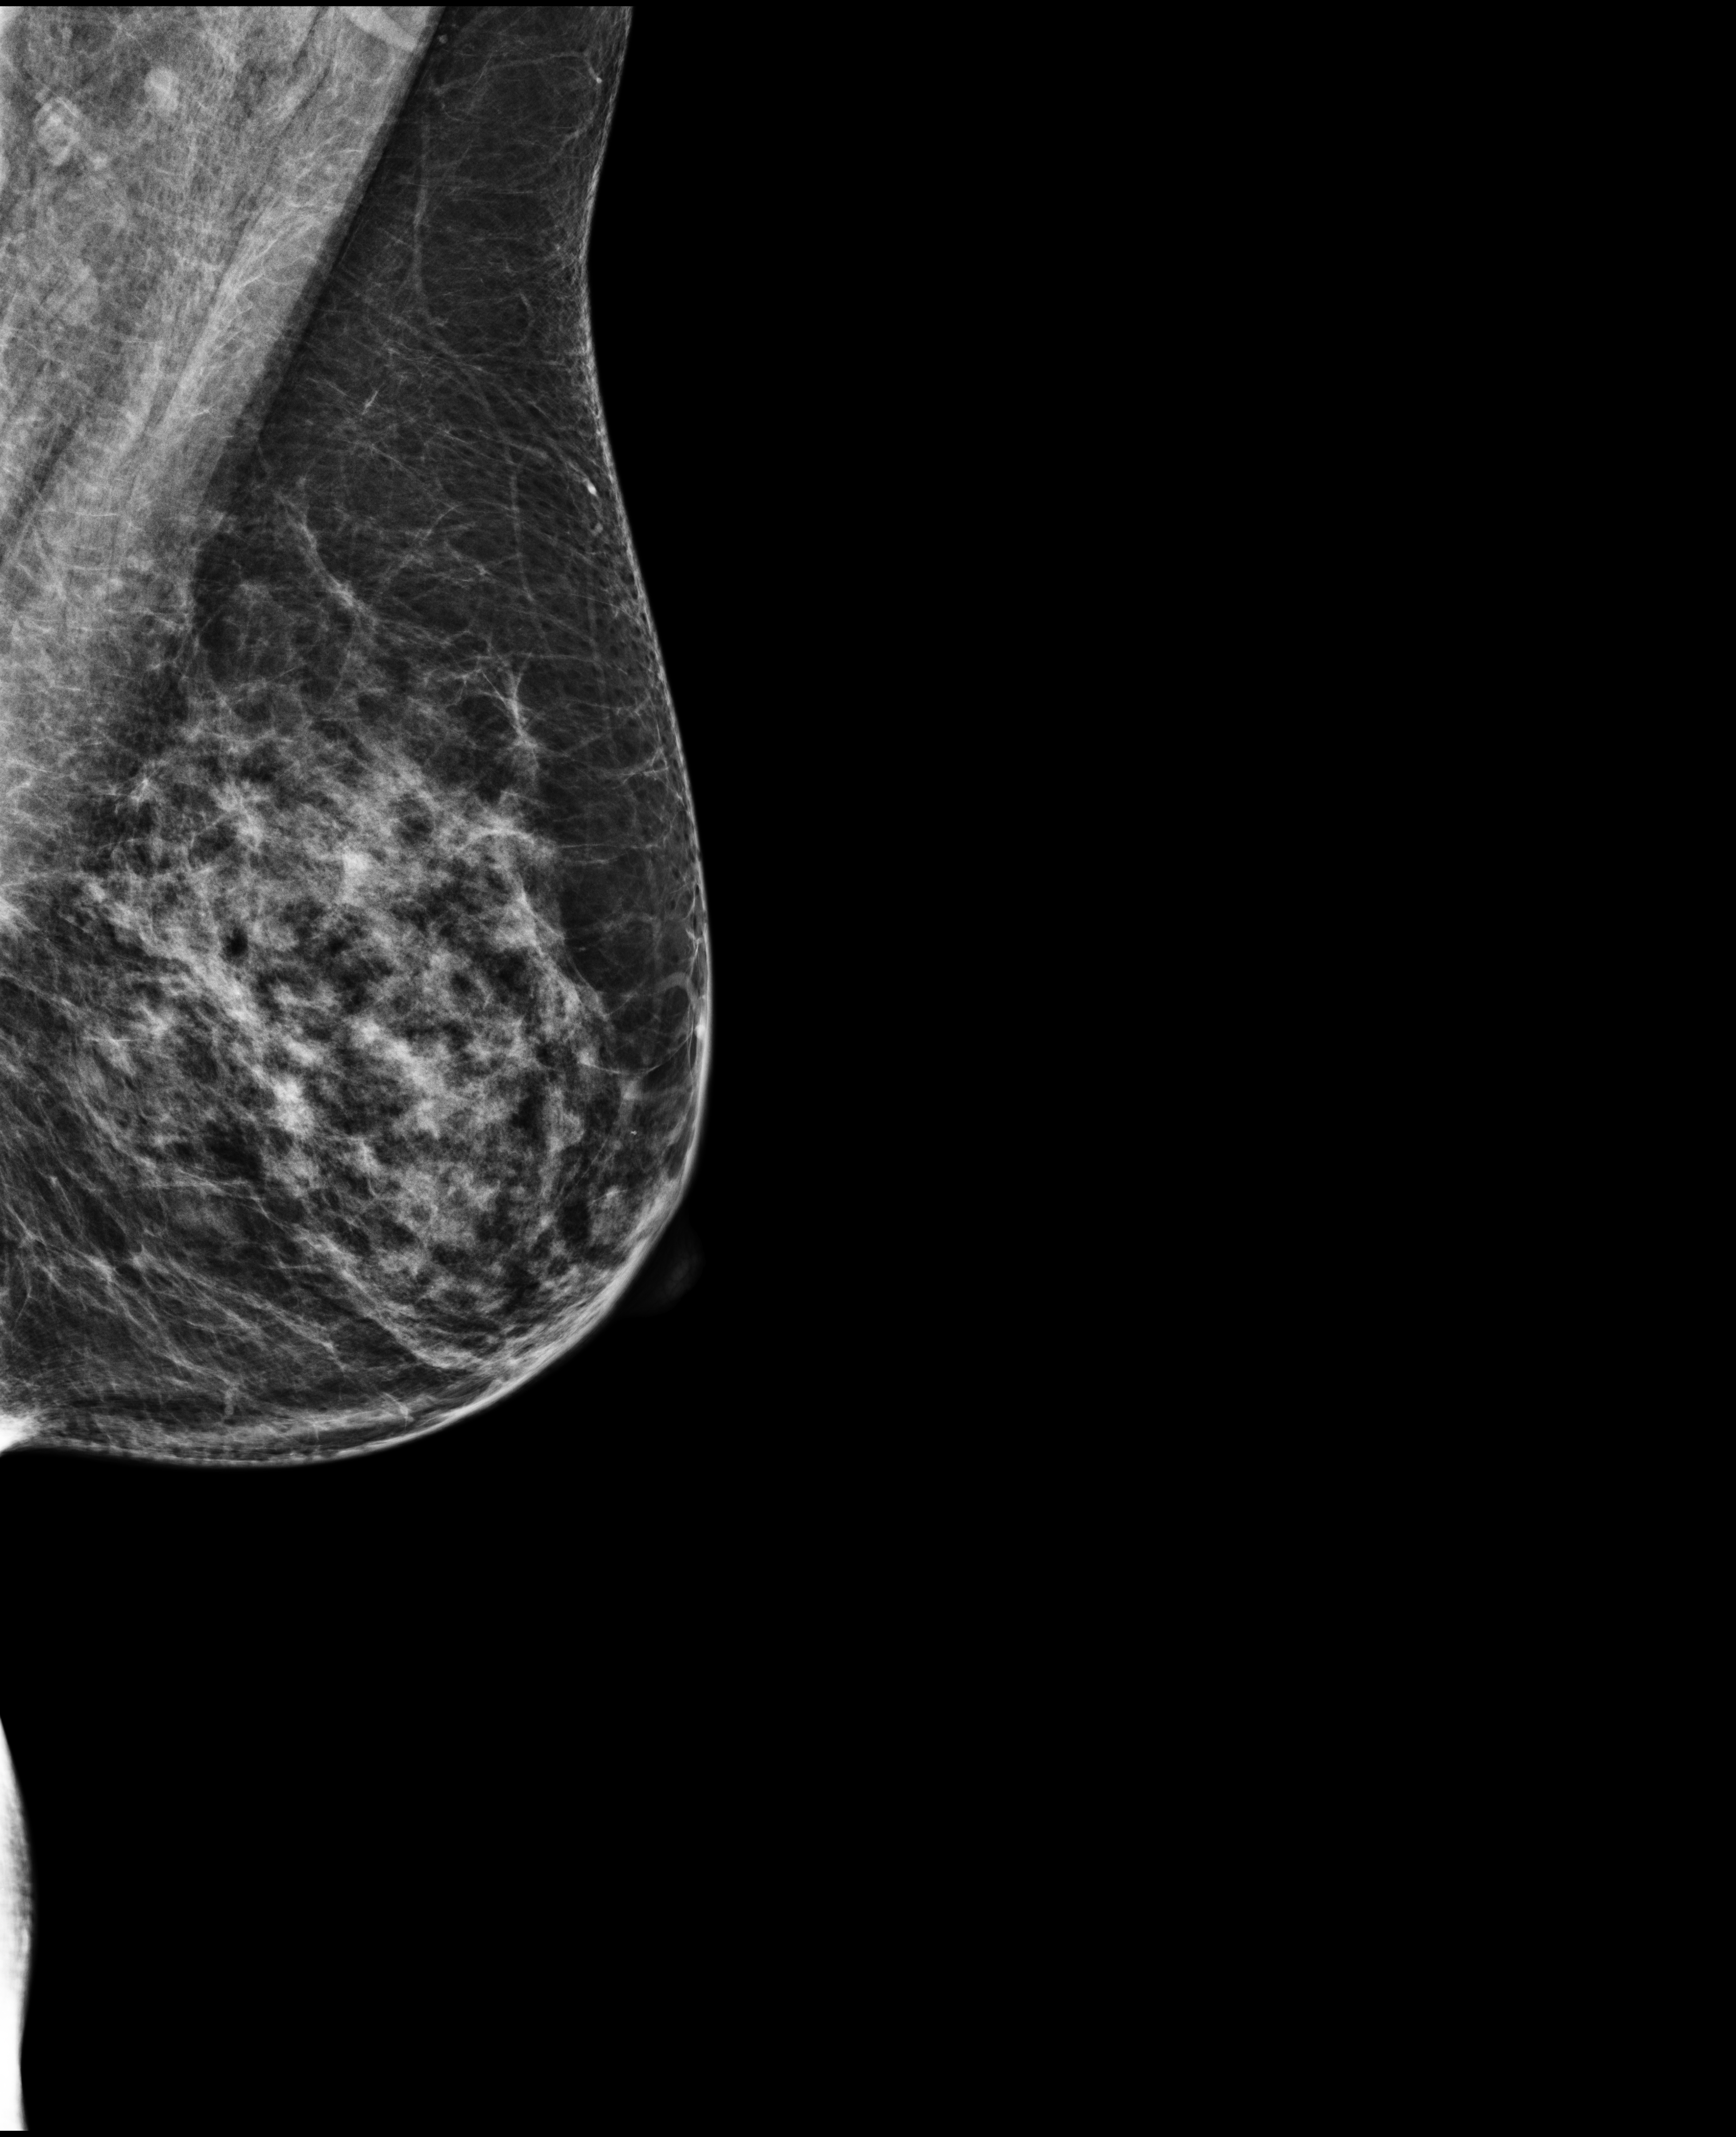
Screening examination; compressed breast thickness 67 mm.
Image type: full-field digital mammogram. Breast: left. Projection: mediolateral oblique (MLO) view.